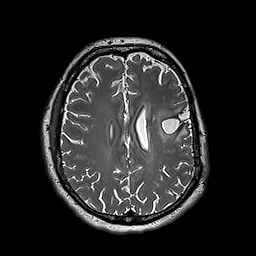
Brain MRI from a brain-tumour surgery series, one axial slice. Slice 79 of 192 in the series (ordered by position). 256 × 256 image matrix. Case-level facts recorded for this patient, not image findings: histopathology: Astrocytoma; WHO grade: 3; IDH mutation: yes.
Structures marked on this image (expert manual segmentation):
- tumour: box from (x=153, y=102) to (x=174, y=142) px